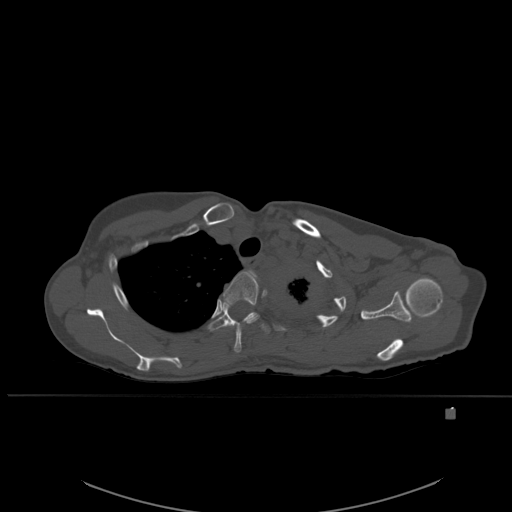
CT including the spine, one axial slice. Position 420 of 537 along the scan axis. Bone window (W 1800 / L 400 HU). 1.5 mm slice thickness. 512 × 512 image matrix, field of view 440 × 440 mm. Female patient, age 45 years. From the clinical record (not read from this slice): primary cancer: lung.
Outlined on this slice (semi-automatically segmented with operator editing):
- T3 vertebra: box from (x=223, y=271) to (x=259, y=353) px
- T4 vertebra: (x=208, y=301)–(x=271, y=334)